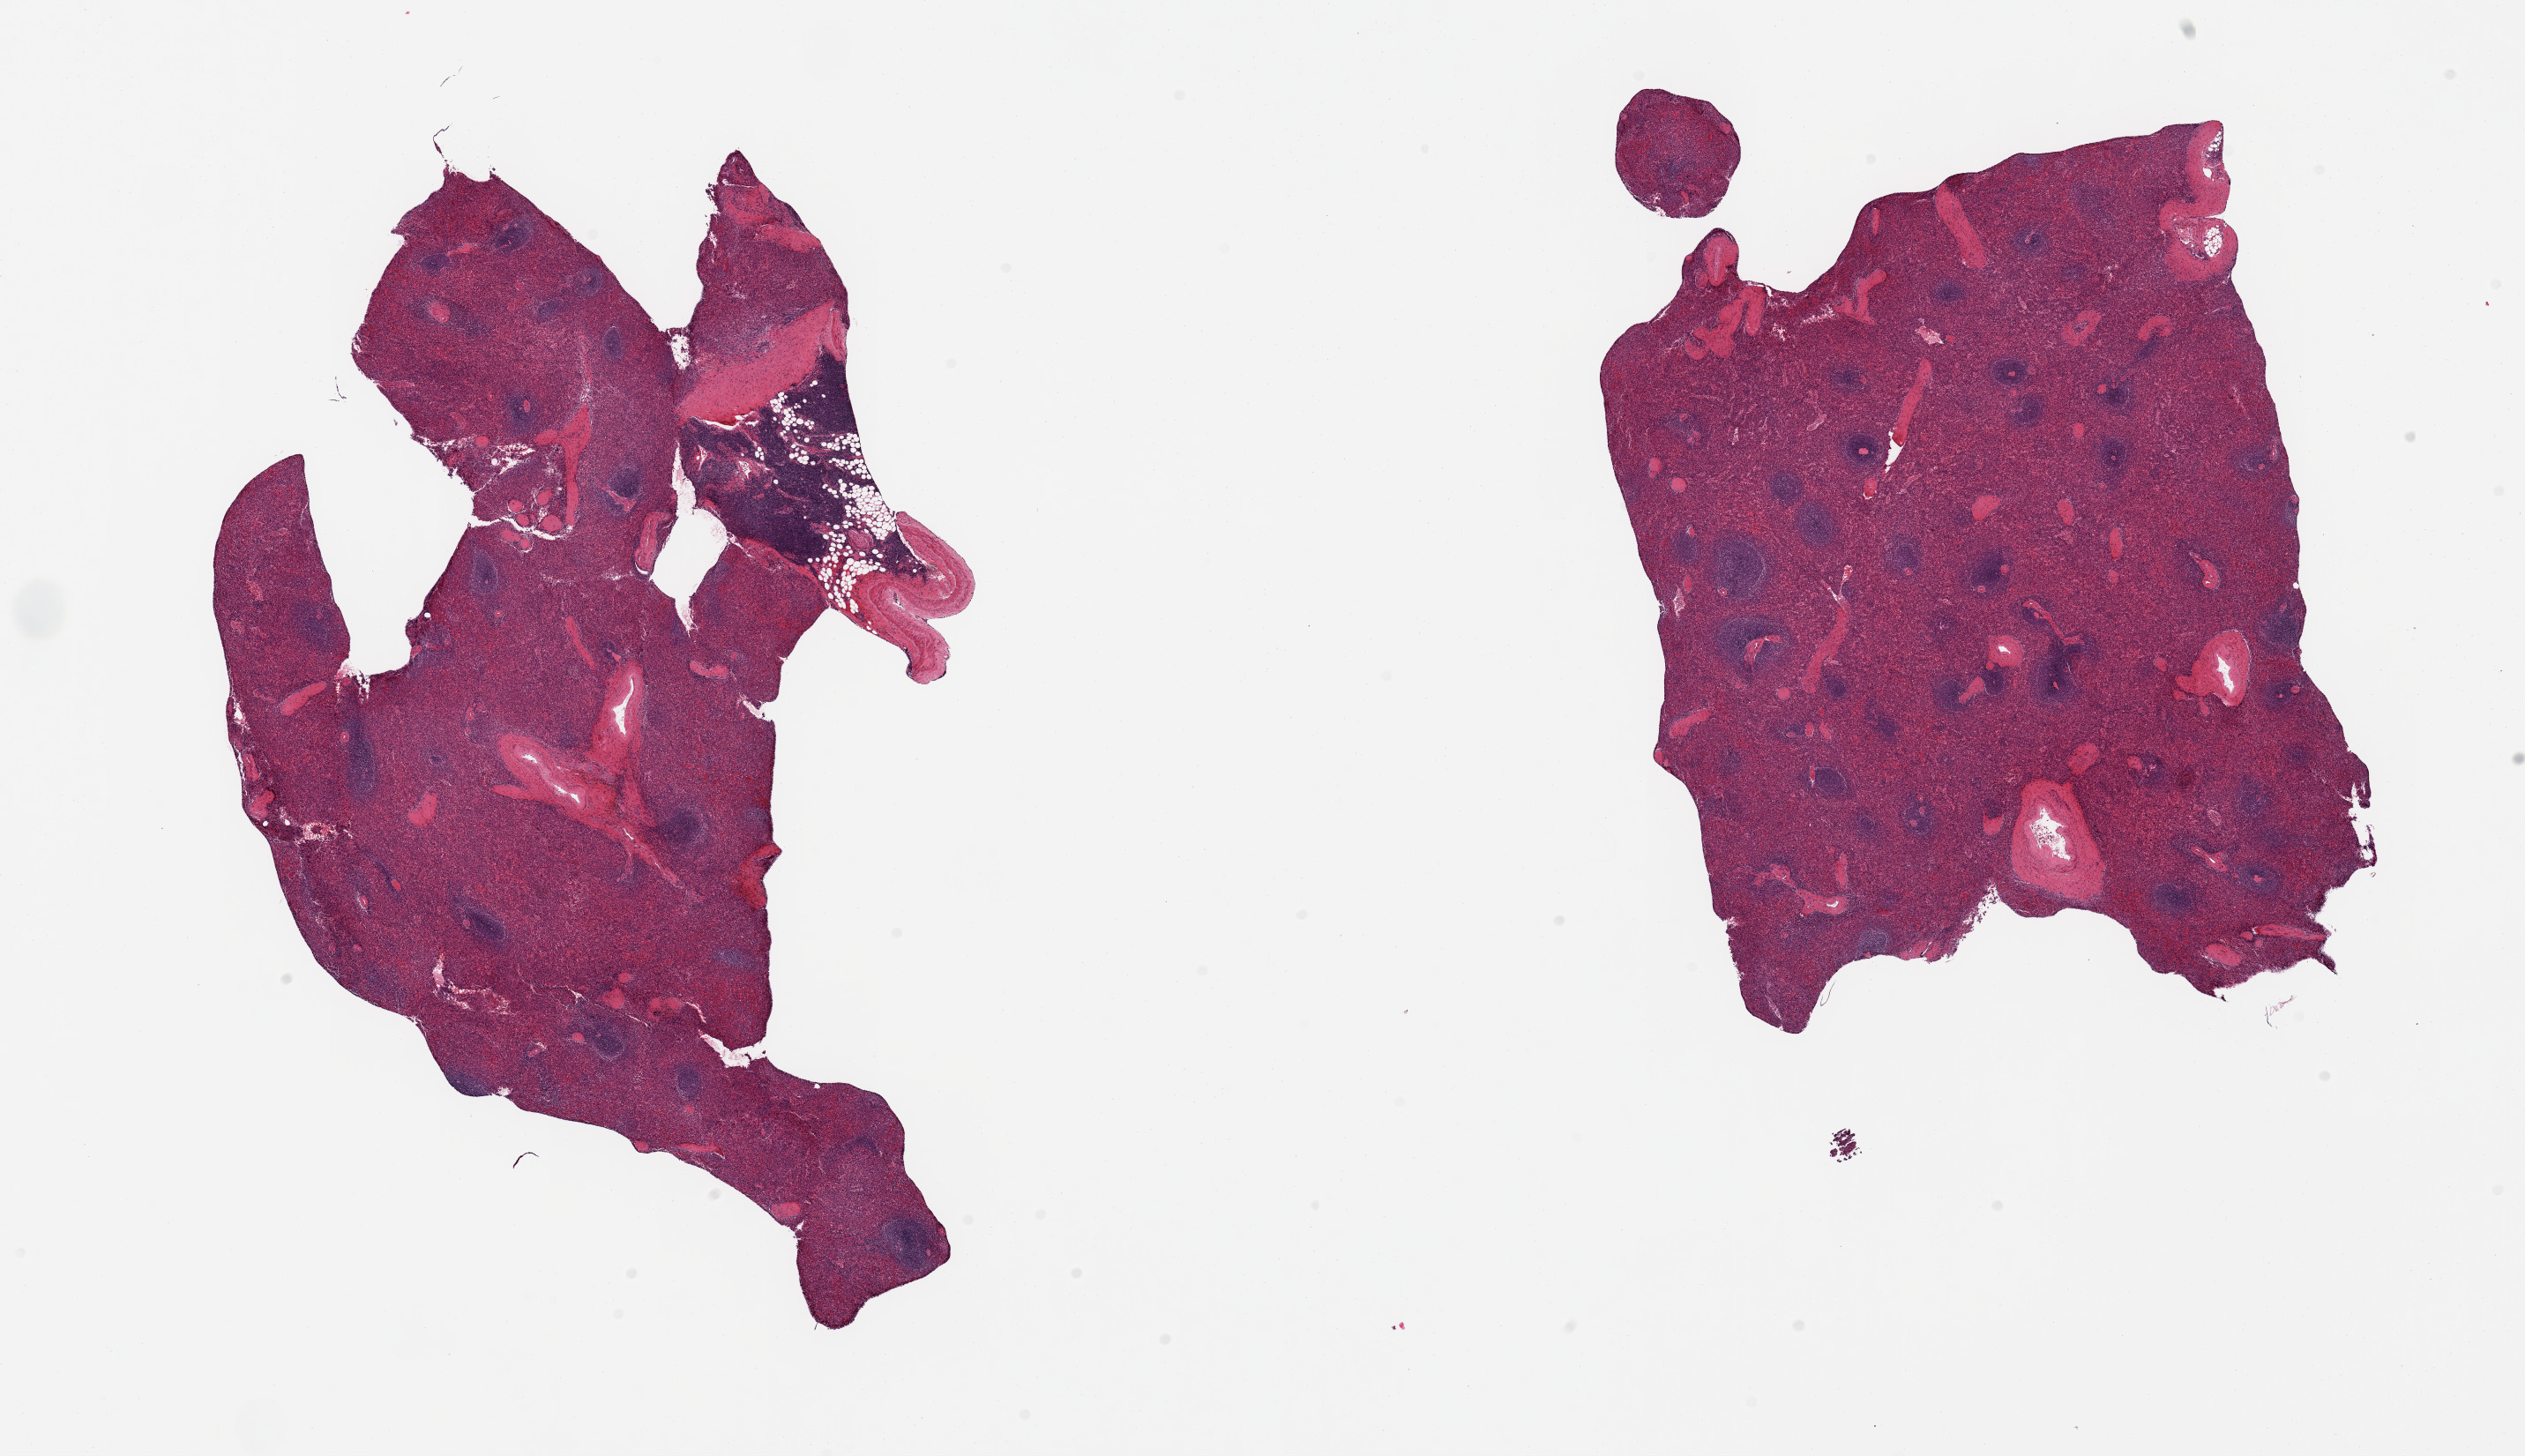
Whole-slide image, haematoxylin and eosin stain, shown as a low-resolution overview of the whole scanned area (about 22.6 x 13.1 mm, slide scanned at 20x). PAXgene-fixed, paraffin-embedded tissue. Sampled site (target tissue): spleen. Tissue donor sample. Donor: male.
- review note (as recorded): 2 pieces